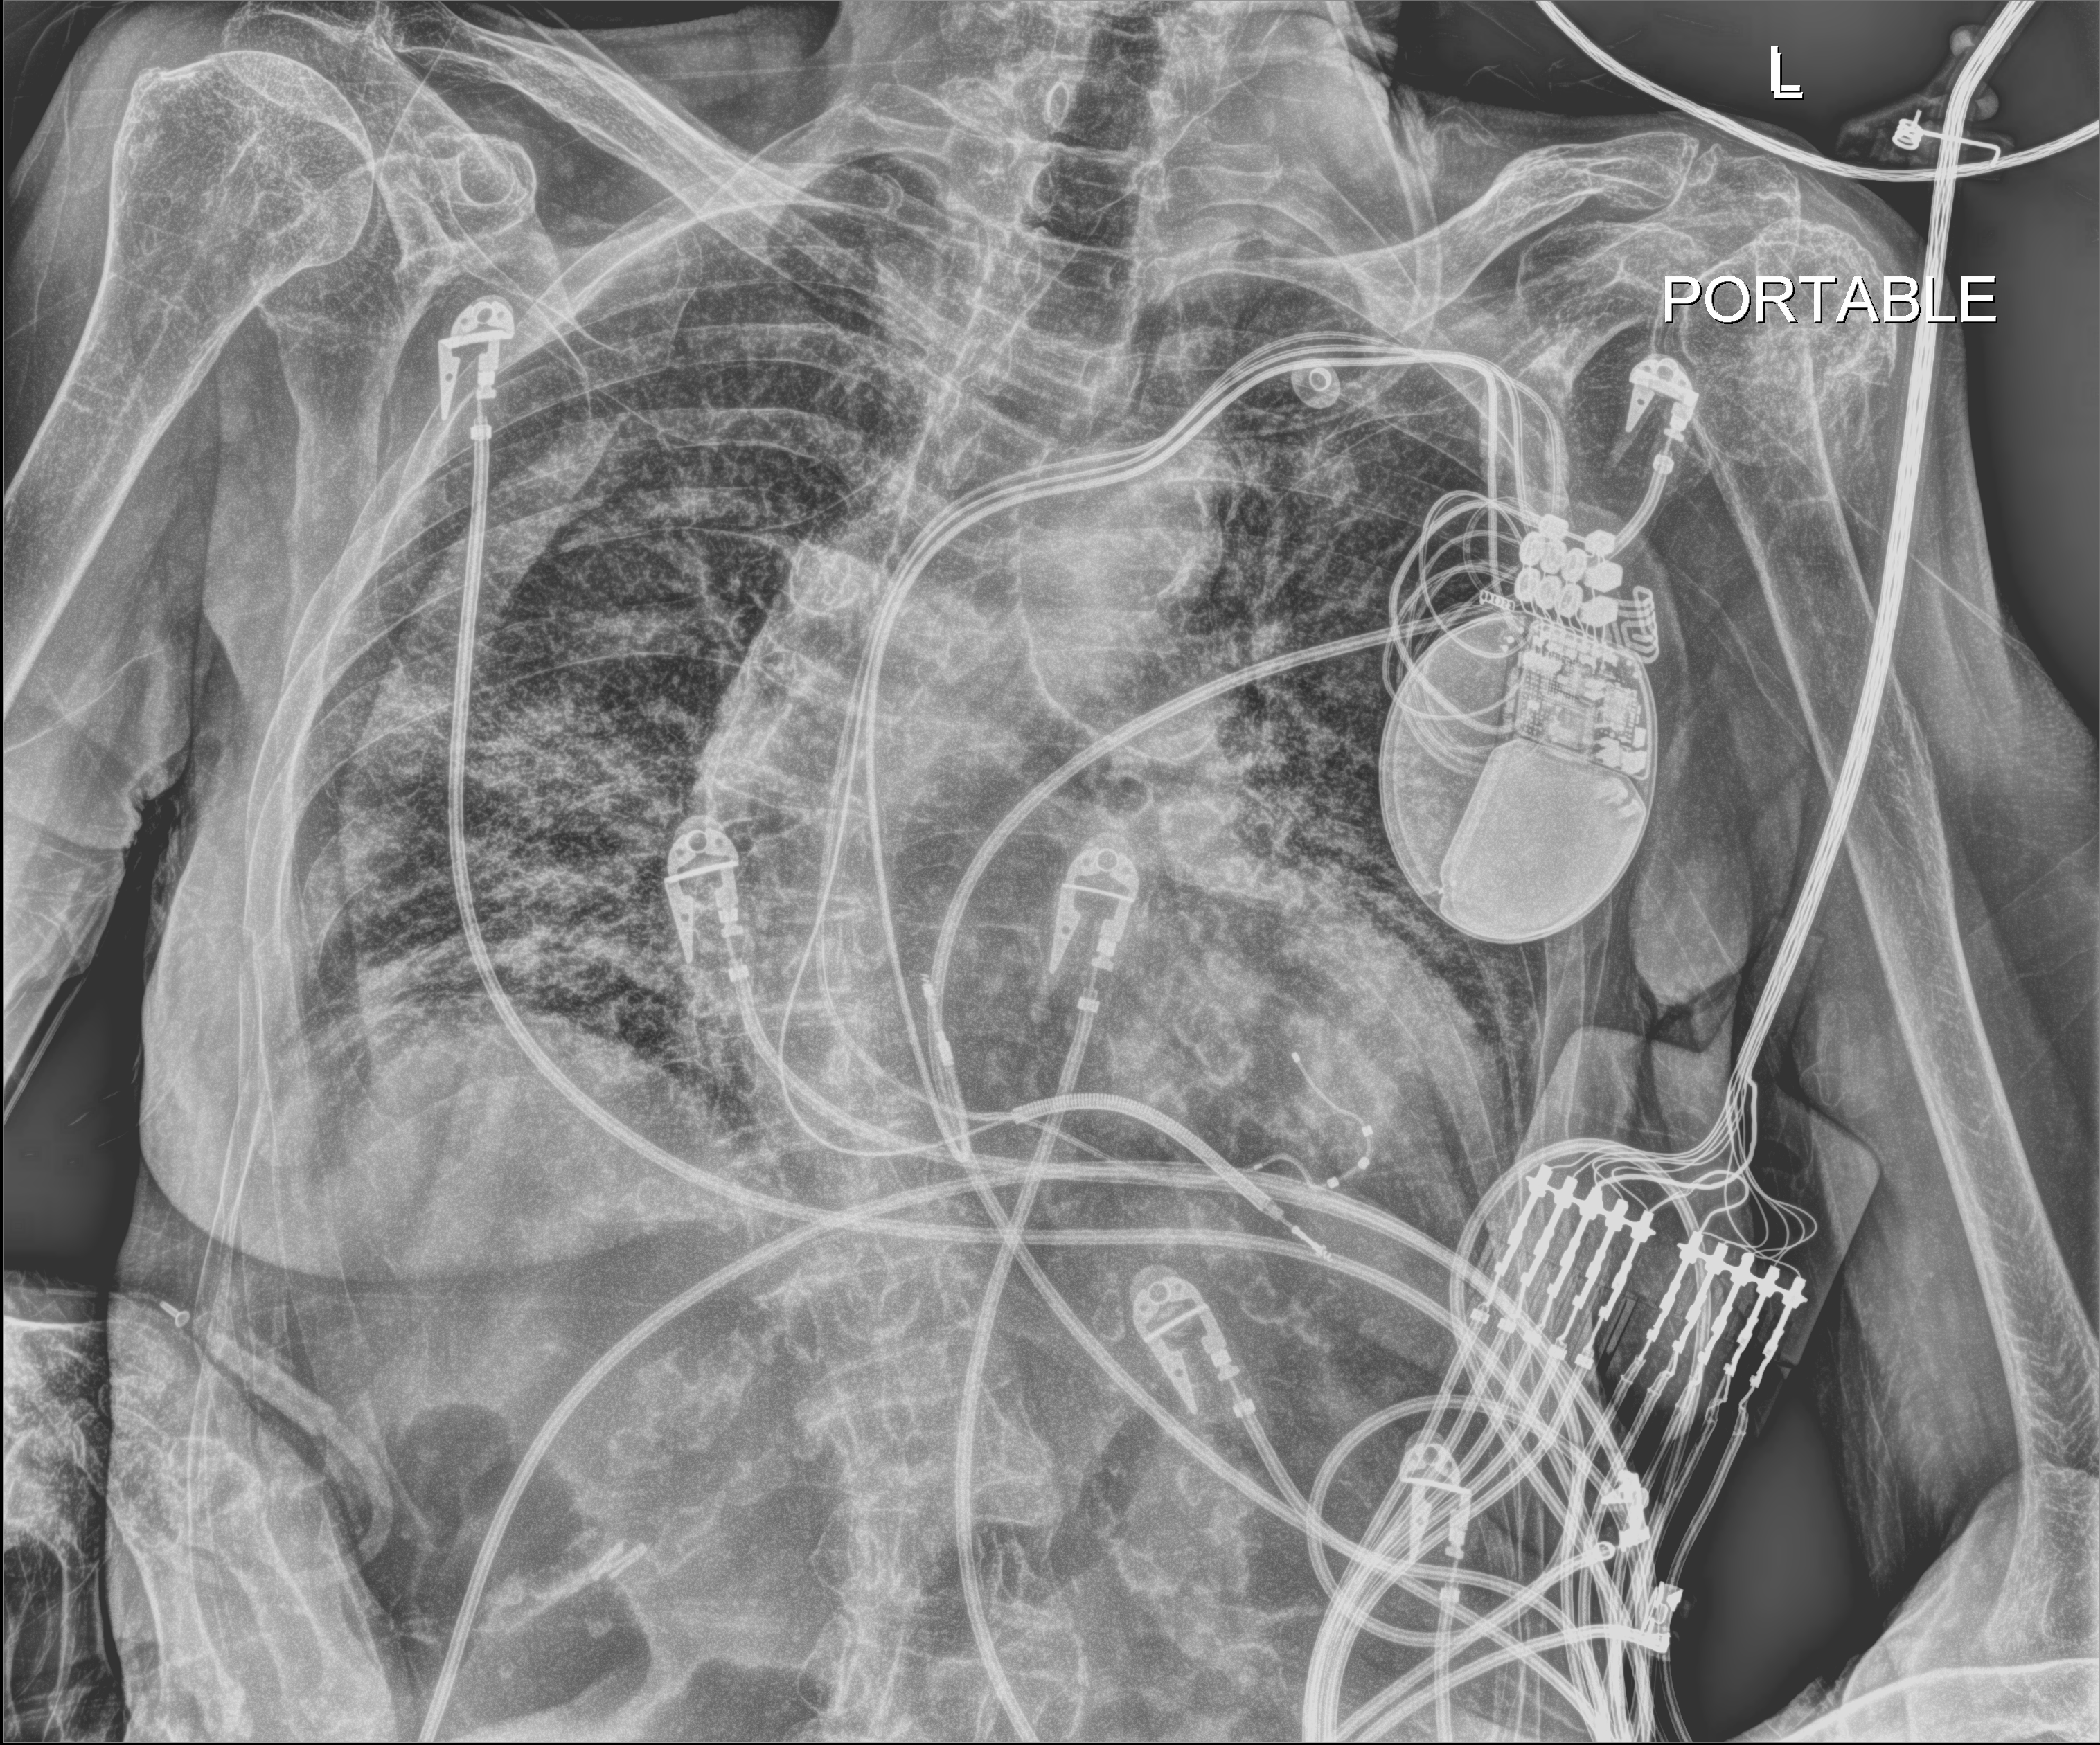
Chest radiograph; anteroposterior (AP) projection. Female patient hospitalised with COVID-19, age 75–90 years.
From the hospital-stay record, not from the radiograph (when in the stay this image was taken is not recorded): admitted to intensive care during this hospital stay: no.